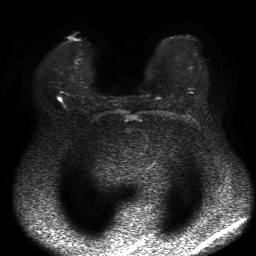
Breast MRI, one axial slice. Position 34 of 50 along the scan axis. Diffusion-weighted series; image 2 of 4 stored at this slice position (different b-values; order by instance number). 1.5 T. 4 mm slice thickness. 256 × 256 image matrix. Female patient.
Outlined on this slice (manually delineated by an expert):
- tumour on diffusion-weighted imaging: bounding box [x1, y1, x2, y2] px = [58, 97, 61, 100]